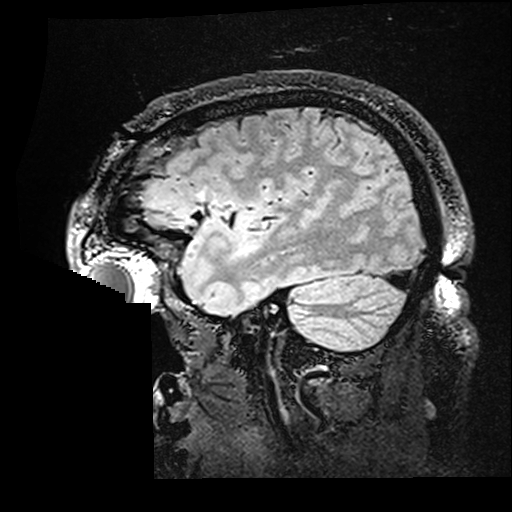
Brain MRI from a brain-tumour surgery series, one sagittal slice. Position 129 of 176 along the scan axis. T2 FLAIR. 512 × 512 image matrix, field of view 250 × 250 mm. From the clinical record (not read from this slice): histopathology: Astrocytoma; WHO grade: 2; IDH mutation: yes; tumour location: Right Insular.
Structures marked on this image (expert manual segmentation):
- residual tumour: box from (x=241, y=239) to (x=256, y=255) px